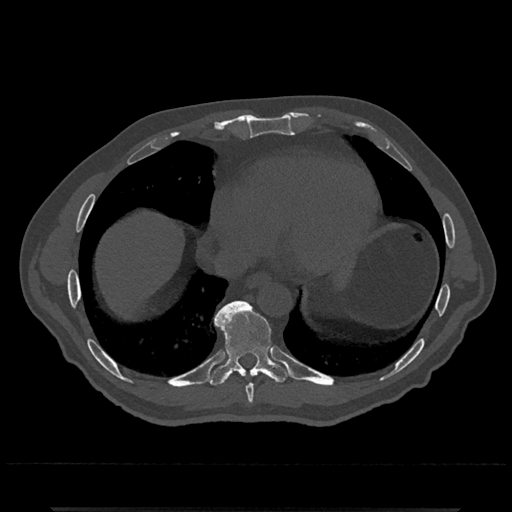
CT including the spine, one axial slice. Position 628 of 797 along the scan axis. 120 kVp. Bone window (W 1800 / L 400 HU). 0.5 mm slice thickness. 512 × 512 image matrix, field of view 393 × 393 mm. Male patient, age 67 years. From the clinical record (not read from this slice): primary cancer: prostate.
Annotated regions visible in this slice (semi-automatic segmentation, software-assisted and operator-edited):
- T8 vertebra: bounding box (x1, y1, x2, y2) in pixels: (246, 384, 254, 404)
- T9 vertebra: (207, 301, 292, 387)